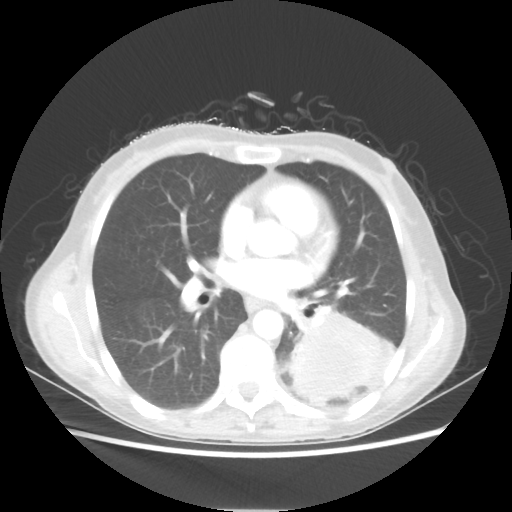
Chest CT, one axial slice. Position 28 of 56 along the scan axis. Reconstruction kernel STANDARD. Lung window (W 1500 / L -600 HU). 5 mm slice thickness. 512 × 512 image matrix. Patient: female, 53 years. From the clinical record (not read from this slice): clinical TNM (as recorded): T3 N0 M0.
Structures marked on this image (bounding box drawn by a radiologist):
- lung tumour (recorded histology: adenocarcinoma): bounding box (x1, y1, x2, y2) in pixels: (288, 306, 396, 406)